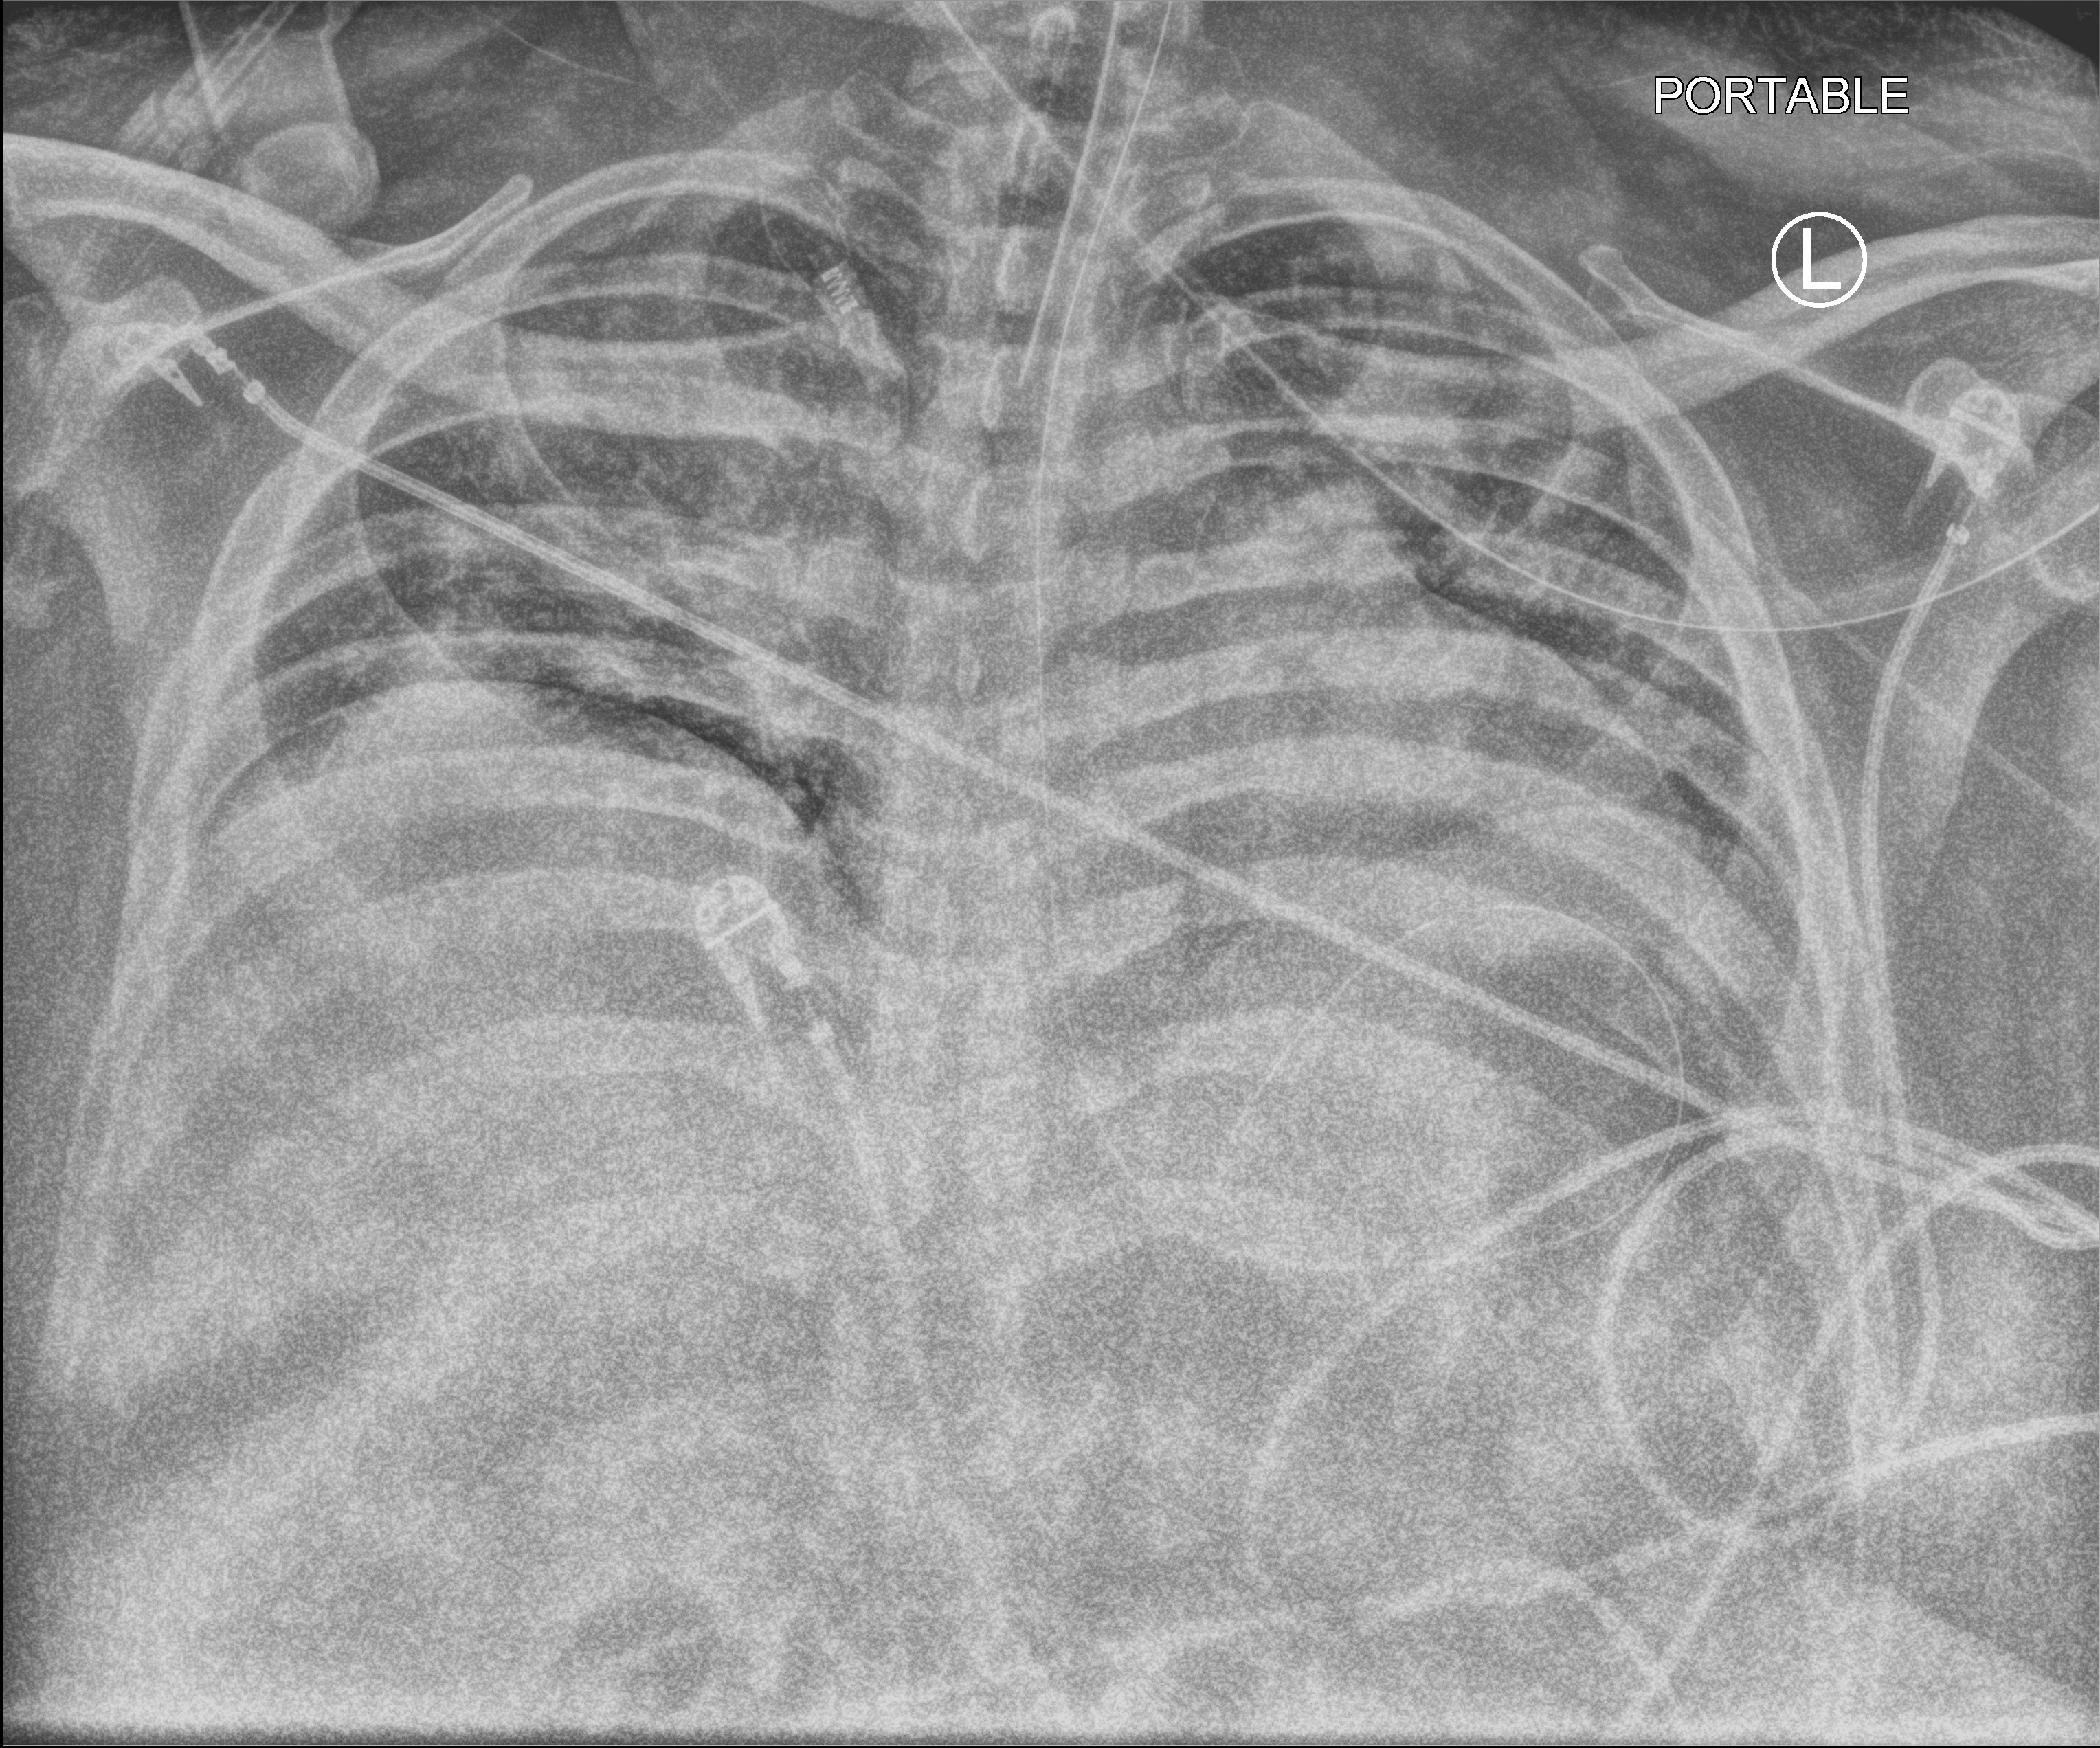
Portable chest radiograph, anteroposterior (AP) projection. Male patient hospitalised with COVID-19, age 18–59 years.
Hospital-stay facts (about this admission, not read from this image; timing relative to this image not recorded): admitted to intensive care during this hospital stay: yes; other chronic lung disease (admission record): yes.